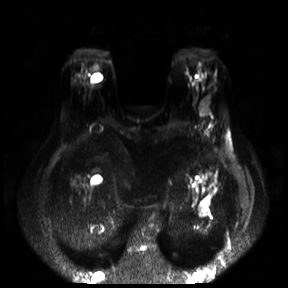
Breast MRI, one axial slice; diffusion-weighted series; image 2 of 4 stored at this slice position (different b-values; order by instance number); 3 T; 4 mm slice thickness; 288 × 288 image matrix, field of view 360 × 360 mm. Female patient.
Annotated regions visible in this slice (manually delineated by an expert):
- tumour on diffusion-weighted imaging: bounding box <199,97,206,114> (left, top, right, bottom; pixels)